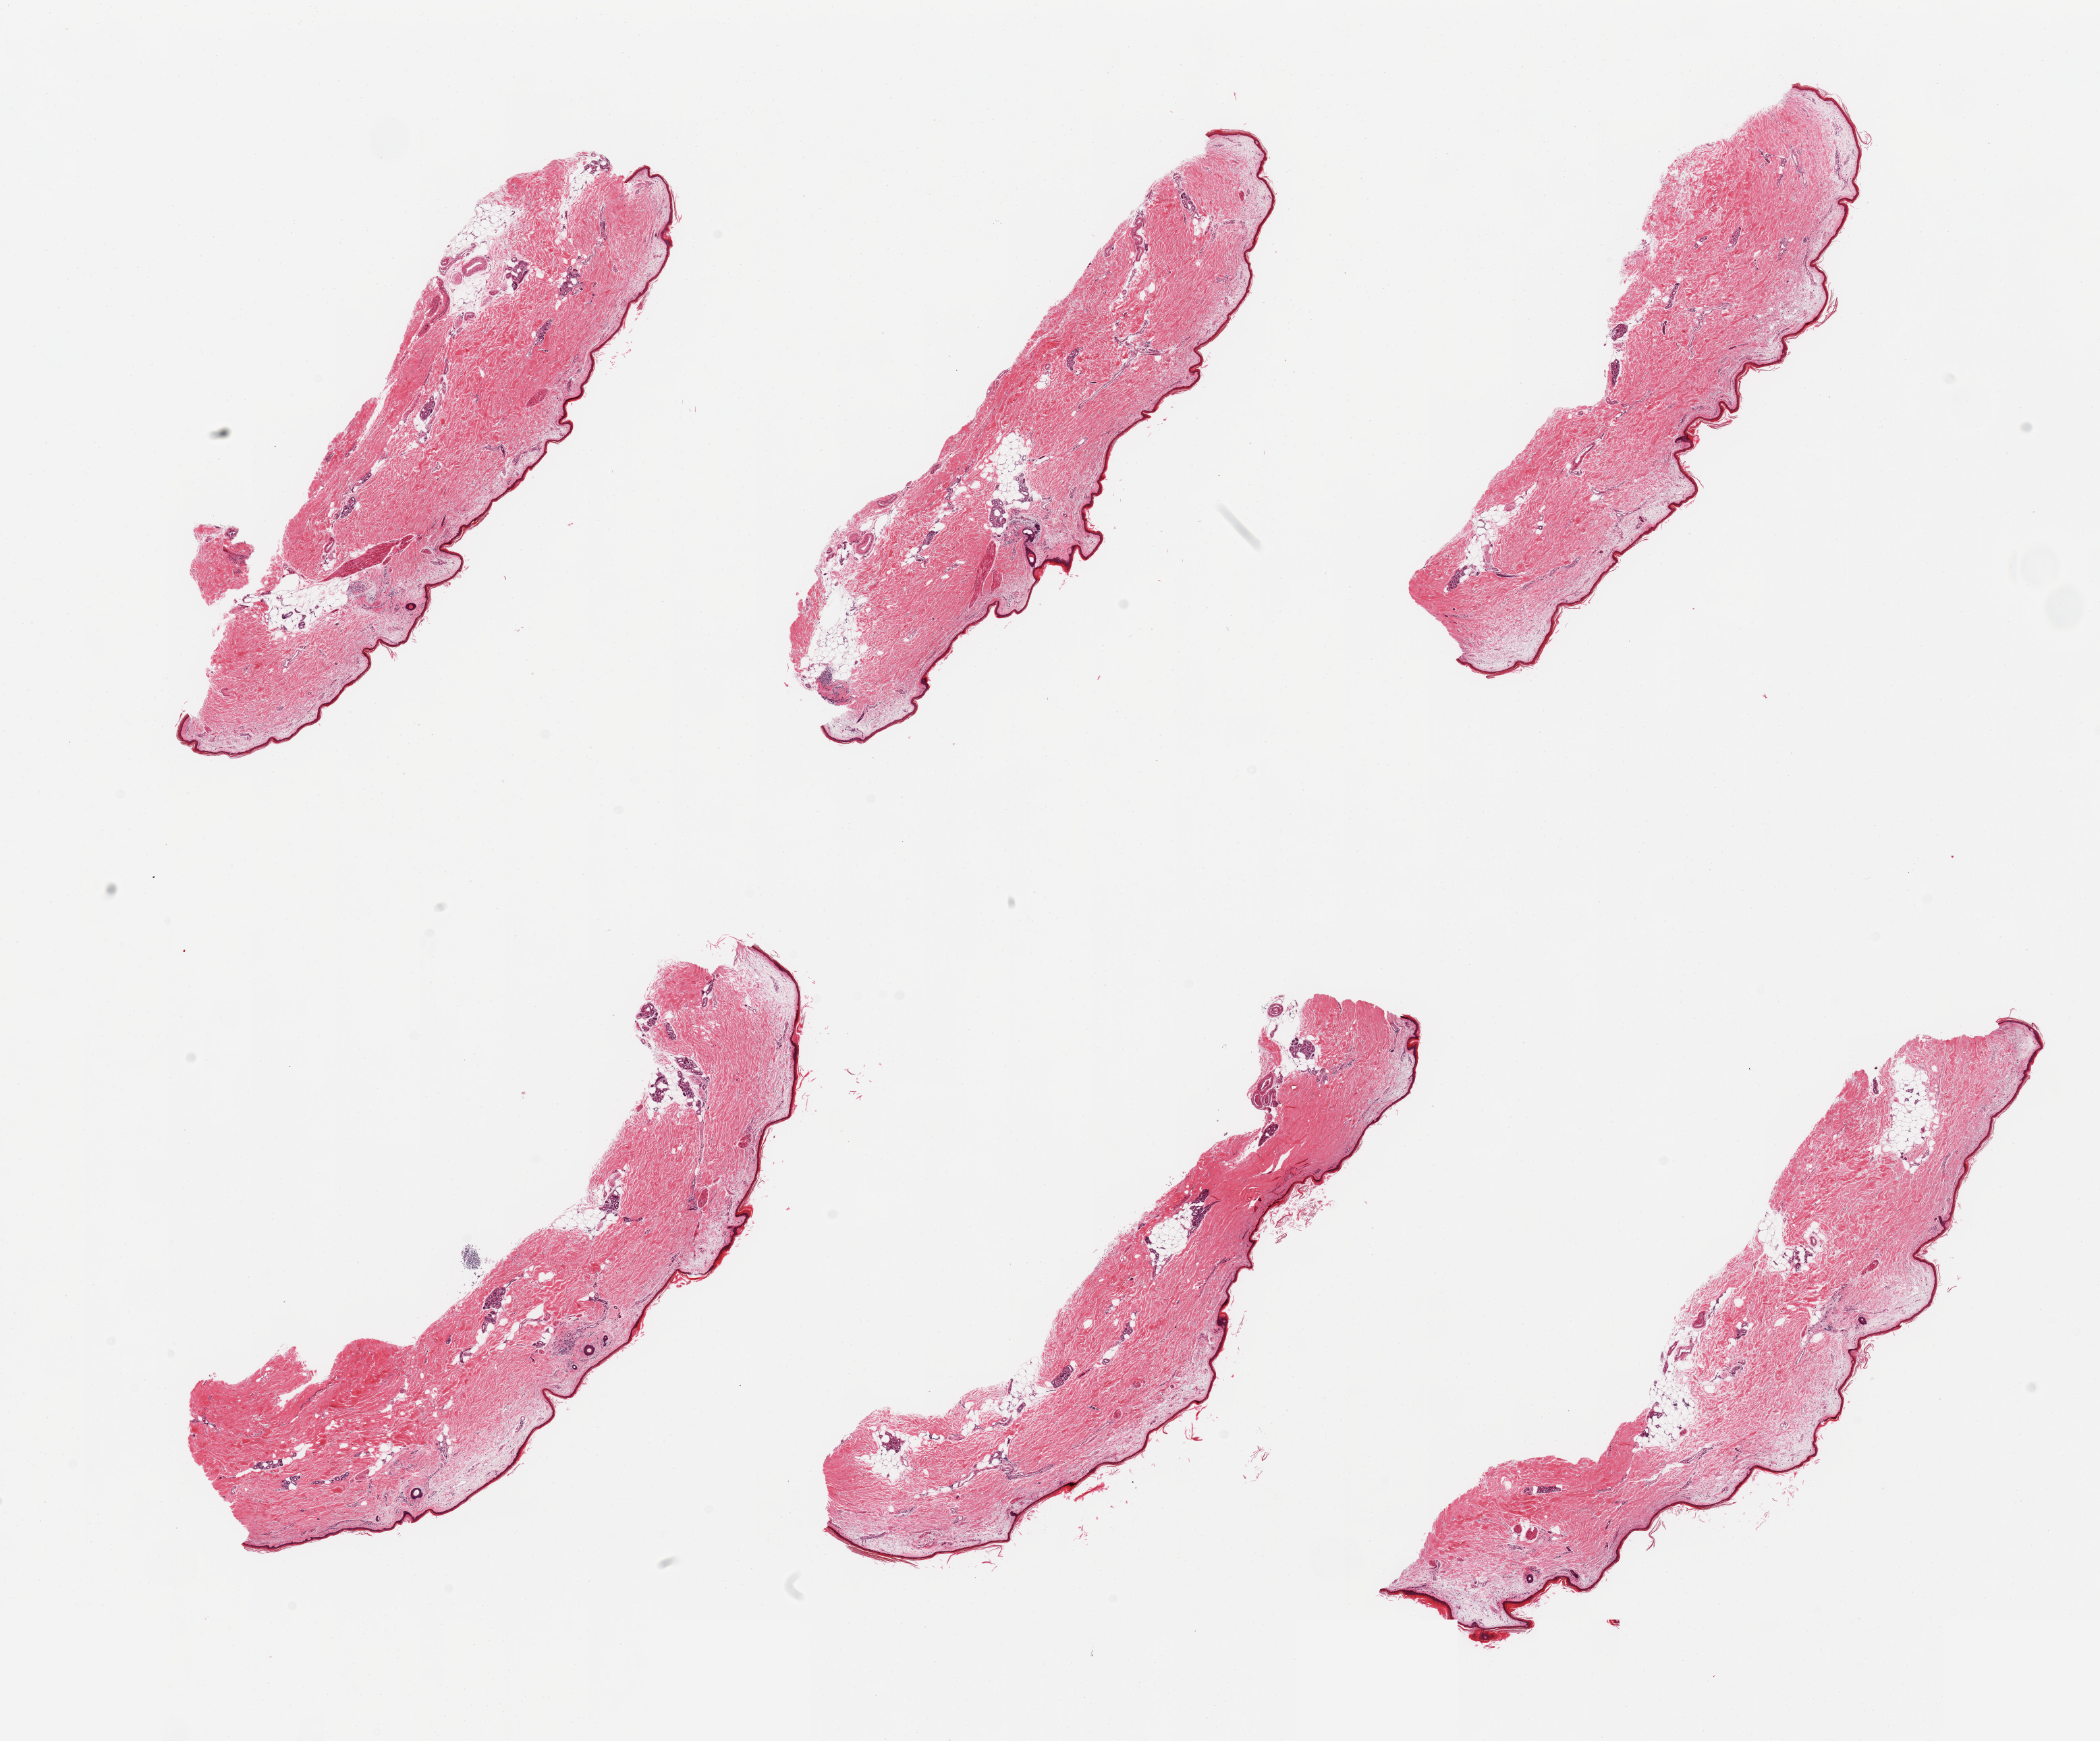
Whole-slide image, haematoxylin and eosin stain — a low-resolution overview of the entire scanned area, about 24.6 x 20.4 mm (slide scanned at 20x); PAXgene-fixed, paraffin-embedded tissue; sampled site (target tissue): skin of lower leg; tissue donor sample. Male donor.
- pathologist's review note for this sample: 6 pieces, edematous dermis, atrophic squamous epithelium (~15-20 microns)